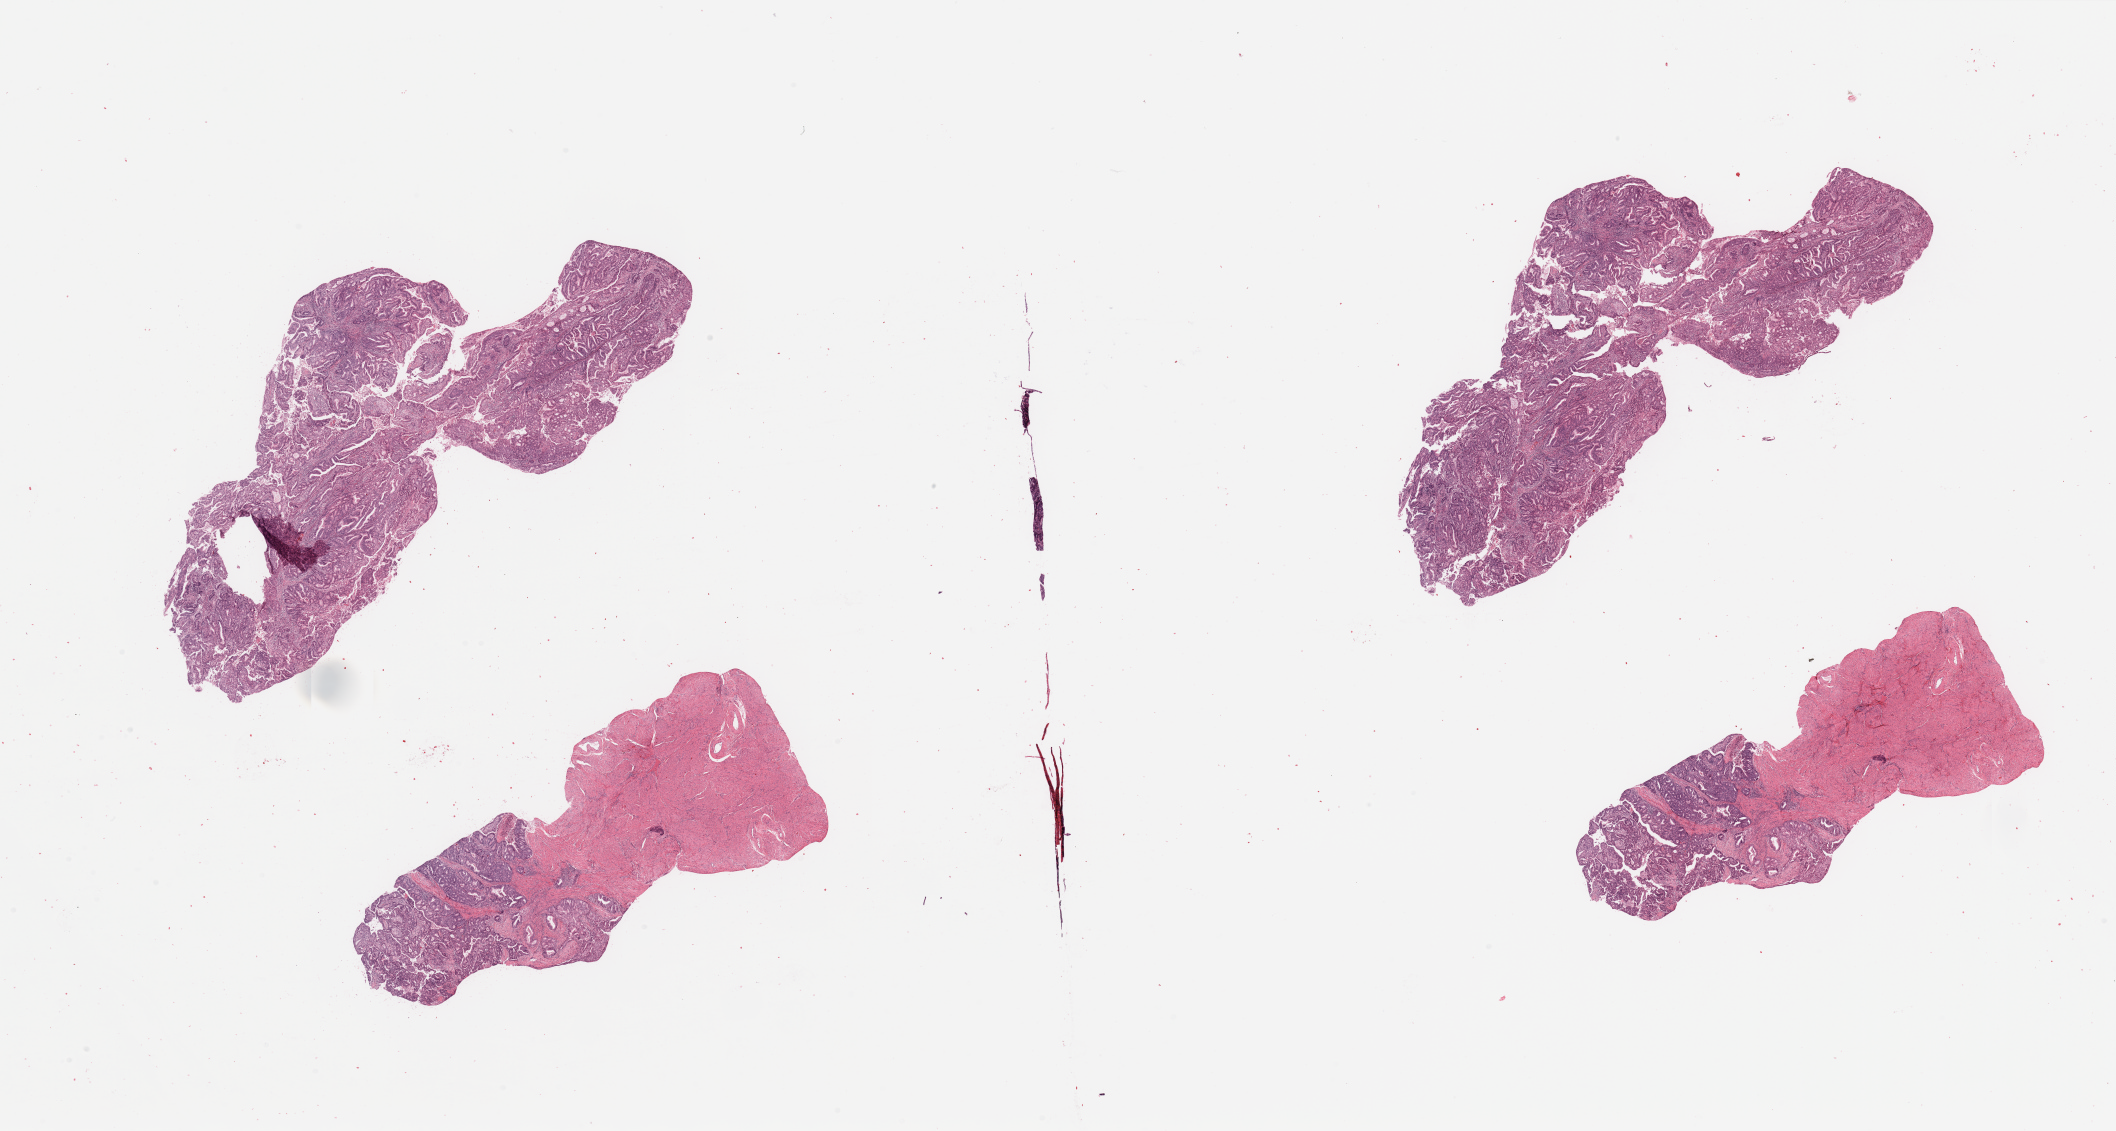
Digitized H&E-stained tissue section (whole slide), low-resolution overview of the scanned area, about 33.5 x 17.9 mm, tumour tissue sample, sampled site: uterus. 51-year-old female patient. Histologic grade: G1 (well differentiated). Slide review estimates, as recorded: tumour nuclei 80%, necrosis 0%.
AJCC pathologic stage: I. Histologic diagnosis: Endometrioid adenocarcinoma, NOS.